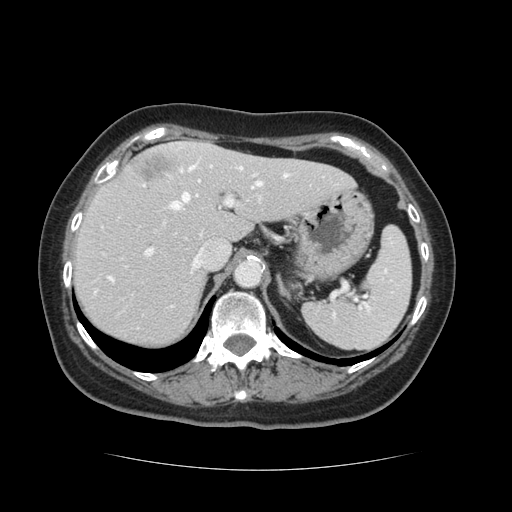
Contrast-enhanced abdominal CT, one axial slice; slice 90 of 128 in the series (ordered by position); 120 kVp; intravenous contrast given; soft-tissue window (W 400 / L 40 HU); 2.5 mm slice thickness; 512 × 512 image matrix, field of view 366 × 366 mm. Female patient, age 67 years. Case-level facts recorded for this patient, not image findings: diagnosis: colorectal cancer liver metastases, imaged before liver resection; multiple liver metastases: yes; largest metastasis: 3 cm; disease in both lobes: yes.
Outlined on this slice (manually delineated by an expert):
- hepatic veins: bounding box (x1, y1, x2, y2) in pixels: (109, 167, 289, 279)
- liver: (74, 144, 351, 348)
- planned liver remnant (the part of the liver to remain after resection): (74, 157, 351, 348)
- portal vein (with intrahepatic branches): (148, 164, 257, 255)
- liver metastasis: (132, 156, 177, 182)